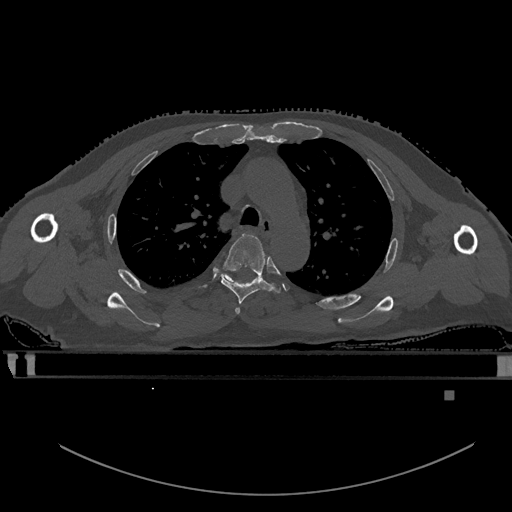
CT including the spine, one axial slice. Position 403 of 969 along the scan axis. Bone window (W 1800 / L 400 HU). 0.5 mm slice thickness. 512 × 512 image matrix. Patient: male, 82 years. From the clinical record (not read from this slice): primary cancer: prostate.
Outlined on this slice (semi-automatically segmented with operator editing):
- T3 vertebra: bounding box [x1, y1, x2, y2] px = [235, 308, 241, 314]
- T4 vertebra: [220, 233, 280, 304]
- T5 vertebra: [216, 272, 237, 283]